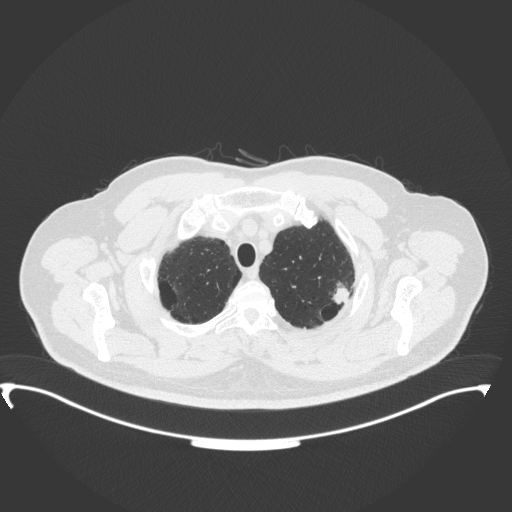
Chest CT, one axial slice; slice 319 of 350 in the series (ordered by position); lung window (W 1500 / L -600 HU); 1 mm slice thickness; 512 × 512 image matrix, field of view 459 × 459 mm. Male patient, age 64 years. From the clinical record (not read from this slice): clinical TNM (as recorded): T1c N1 M1.
Structures marked on this image (rectangle marked by the reading radiologist):
- lung tumour (recorded histology: adenocarcinoma): bounding box (x1, y1, x2, y2) in pixels: (331, 281, 351, 308)